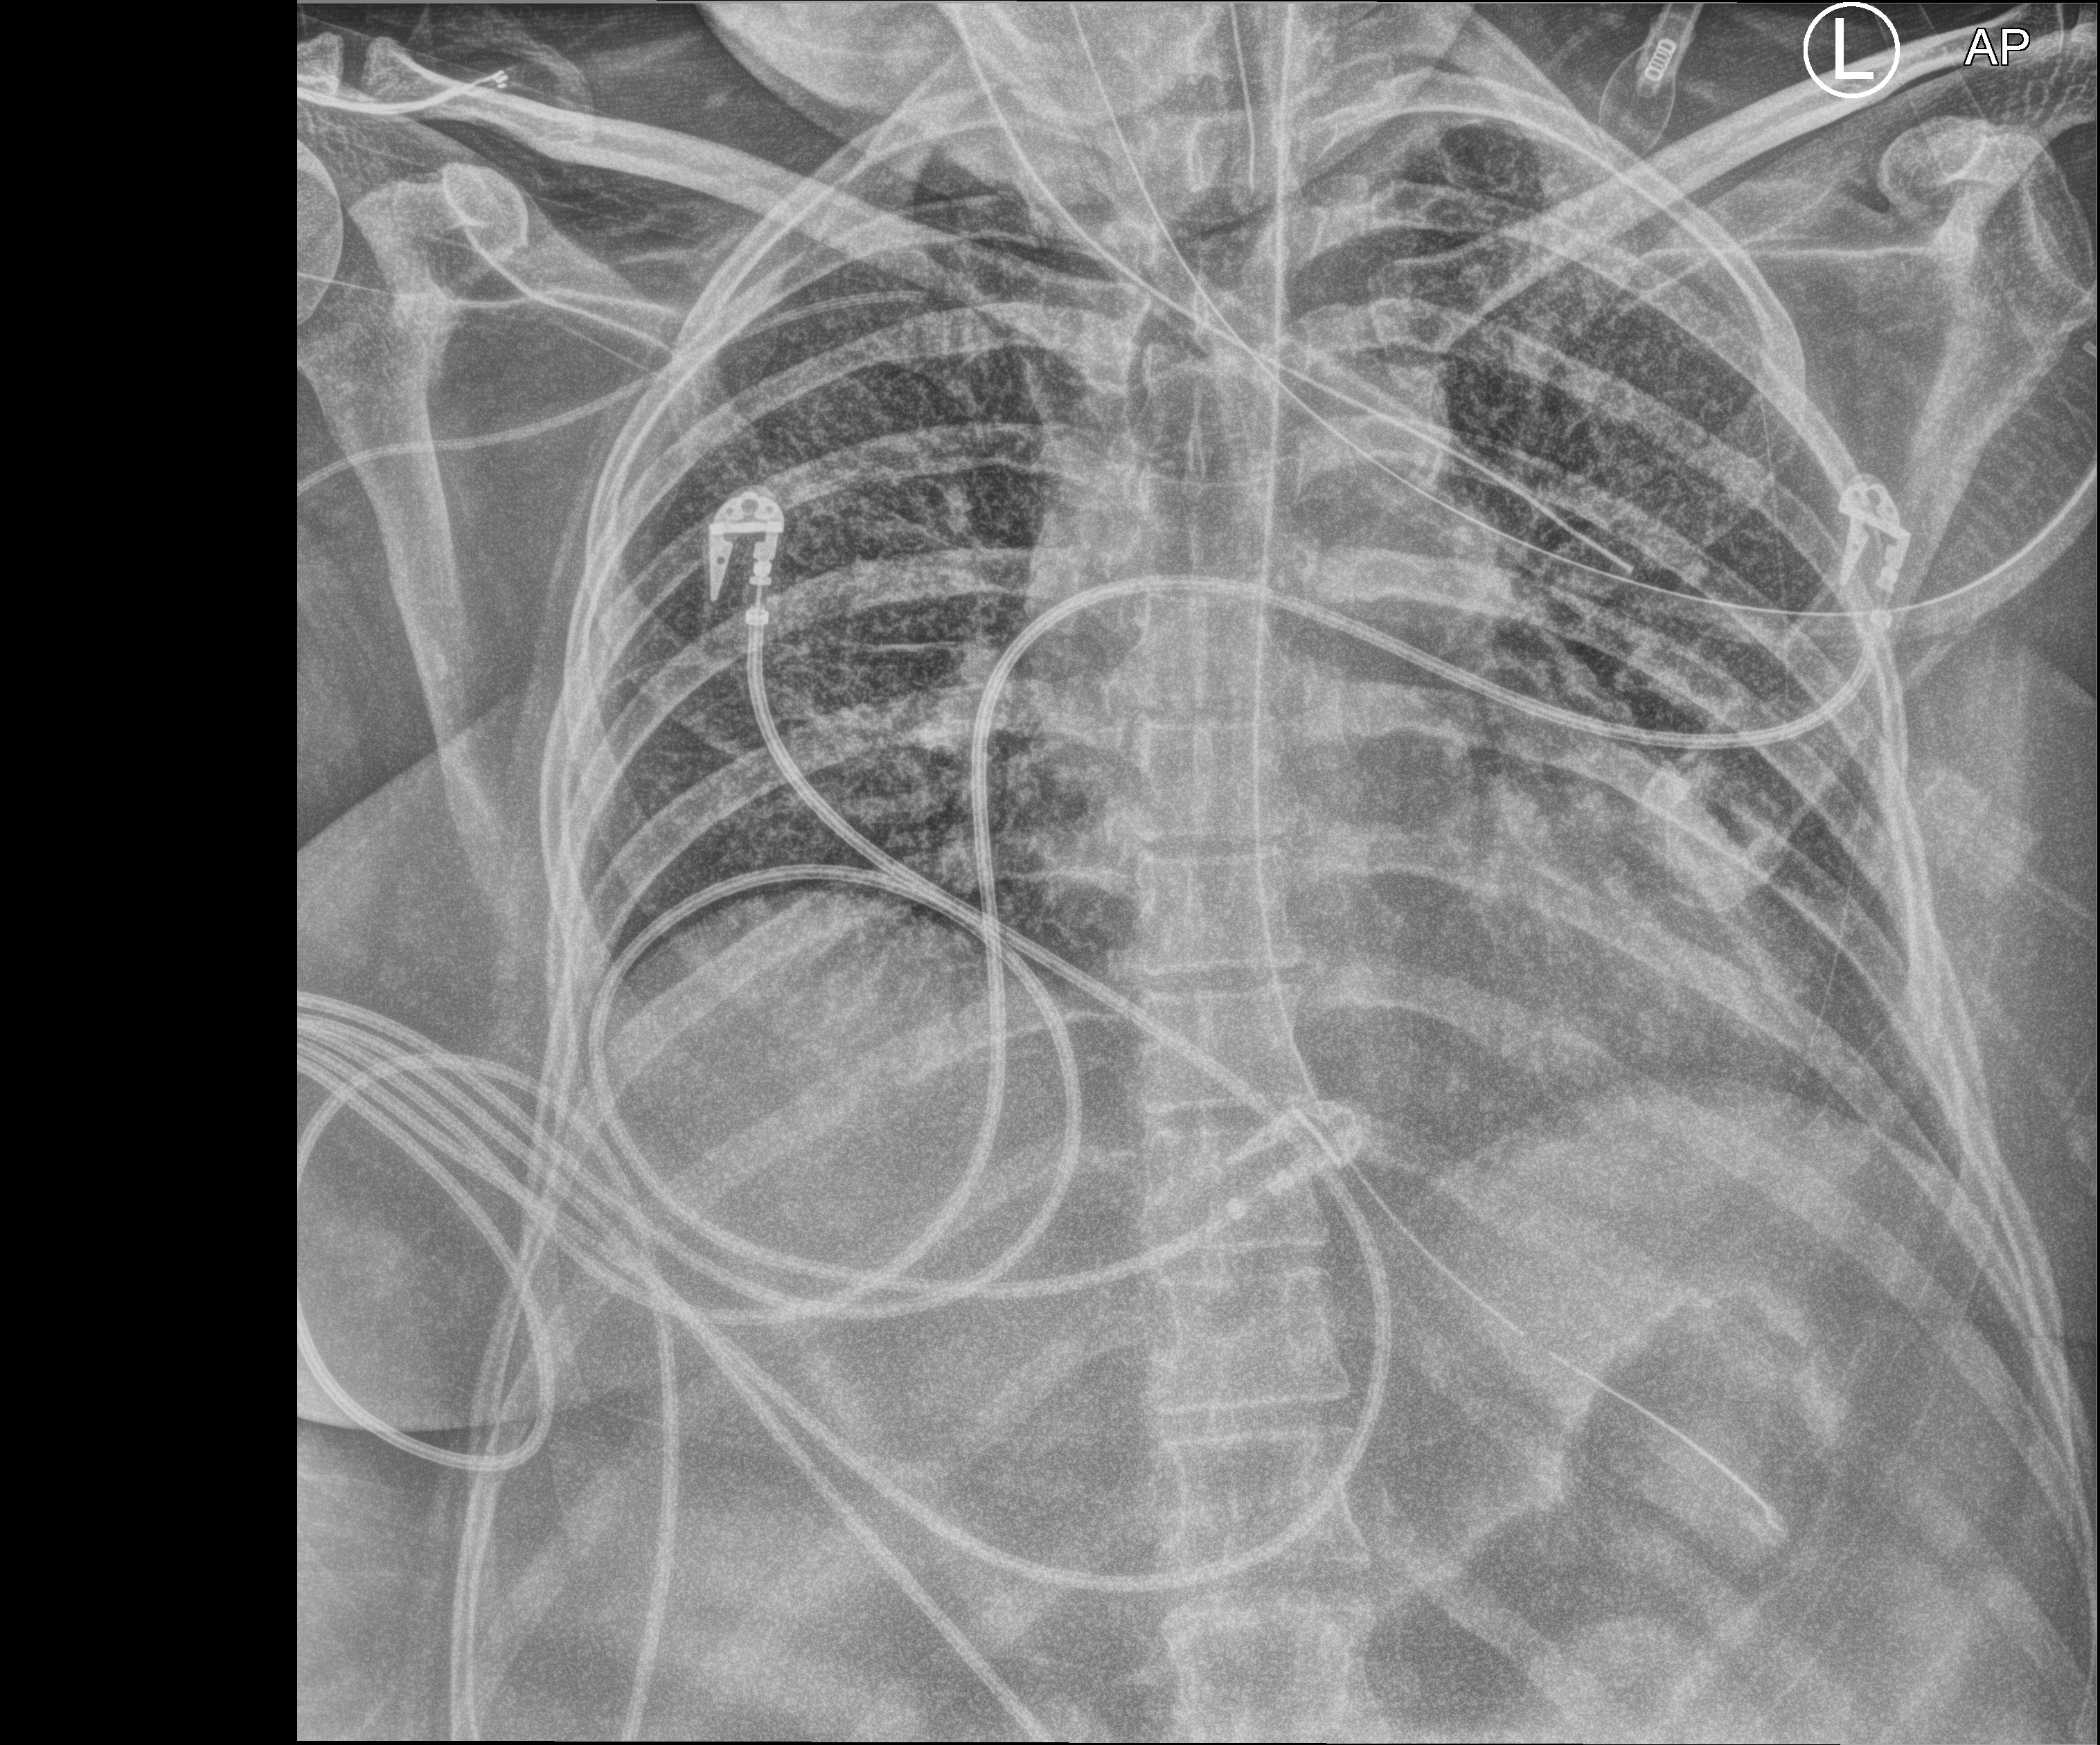
Portable chest radiograph; anteroposterior (AP) projection. Patient hospitalised with COVID-19; female, aged 18–59 years.
Hospital-stay facts (about this admission, not read from this image; timing relative to this image not recorded): admitted to intensive care during this hospital stay: yes.